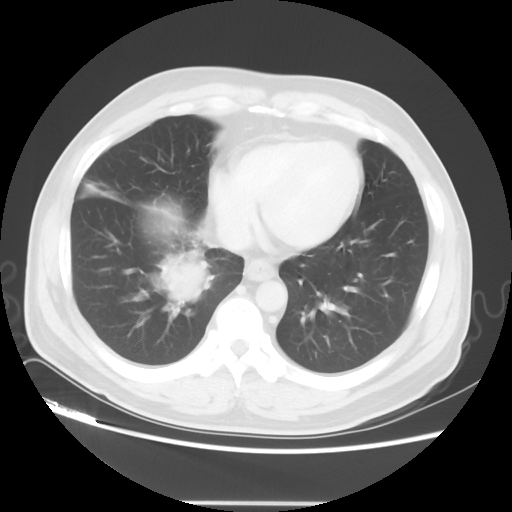
Chest CT, one axial slice; position 15 of 48 along the scan axis; 120 kVp; lung window (W 1500 / L -600 HU); 5 mm slice thickness; 512 × 512 image matrix, field of view 390 × 390 mm. Patient: male, 53 years. Case-level facts recorded for this patient, not image findings: clinical TNM (as recorded): T2 N3 M0.
Outlined on this slice (bounding box drawn by a radiologist):
- lung tumour (recorded histology: small cell carcinoma): box from (x=156, y=254) to (x=213, y=318) px